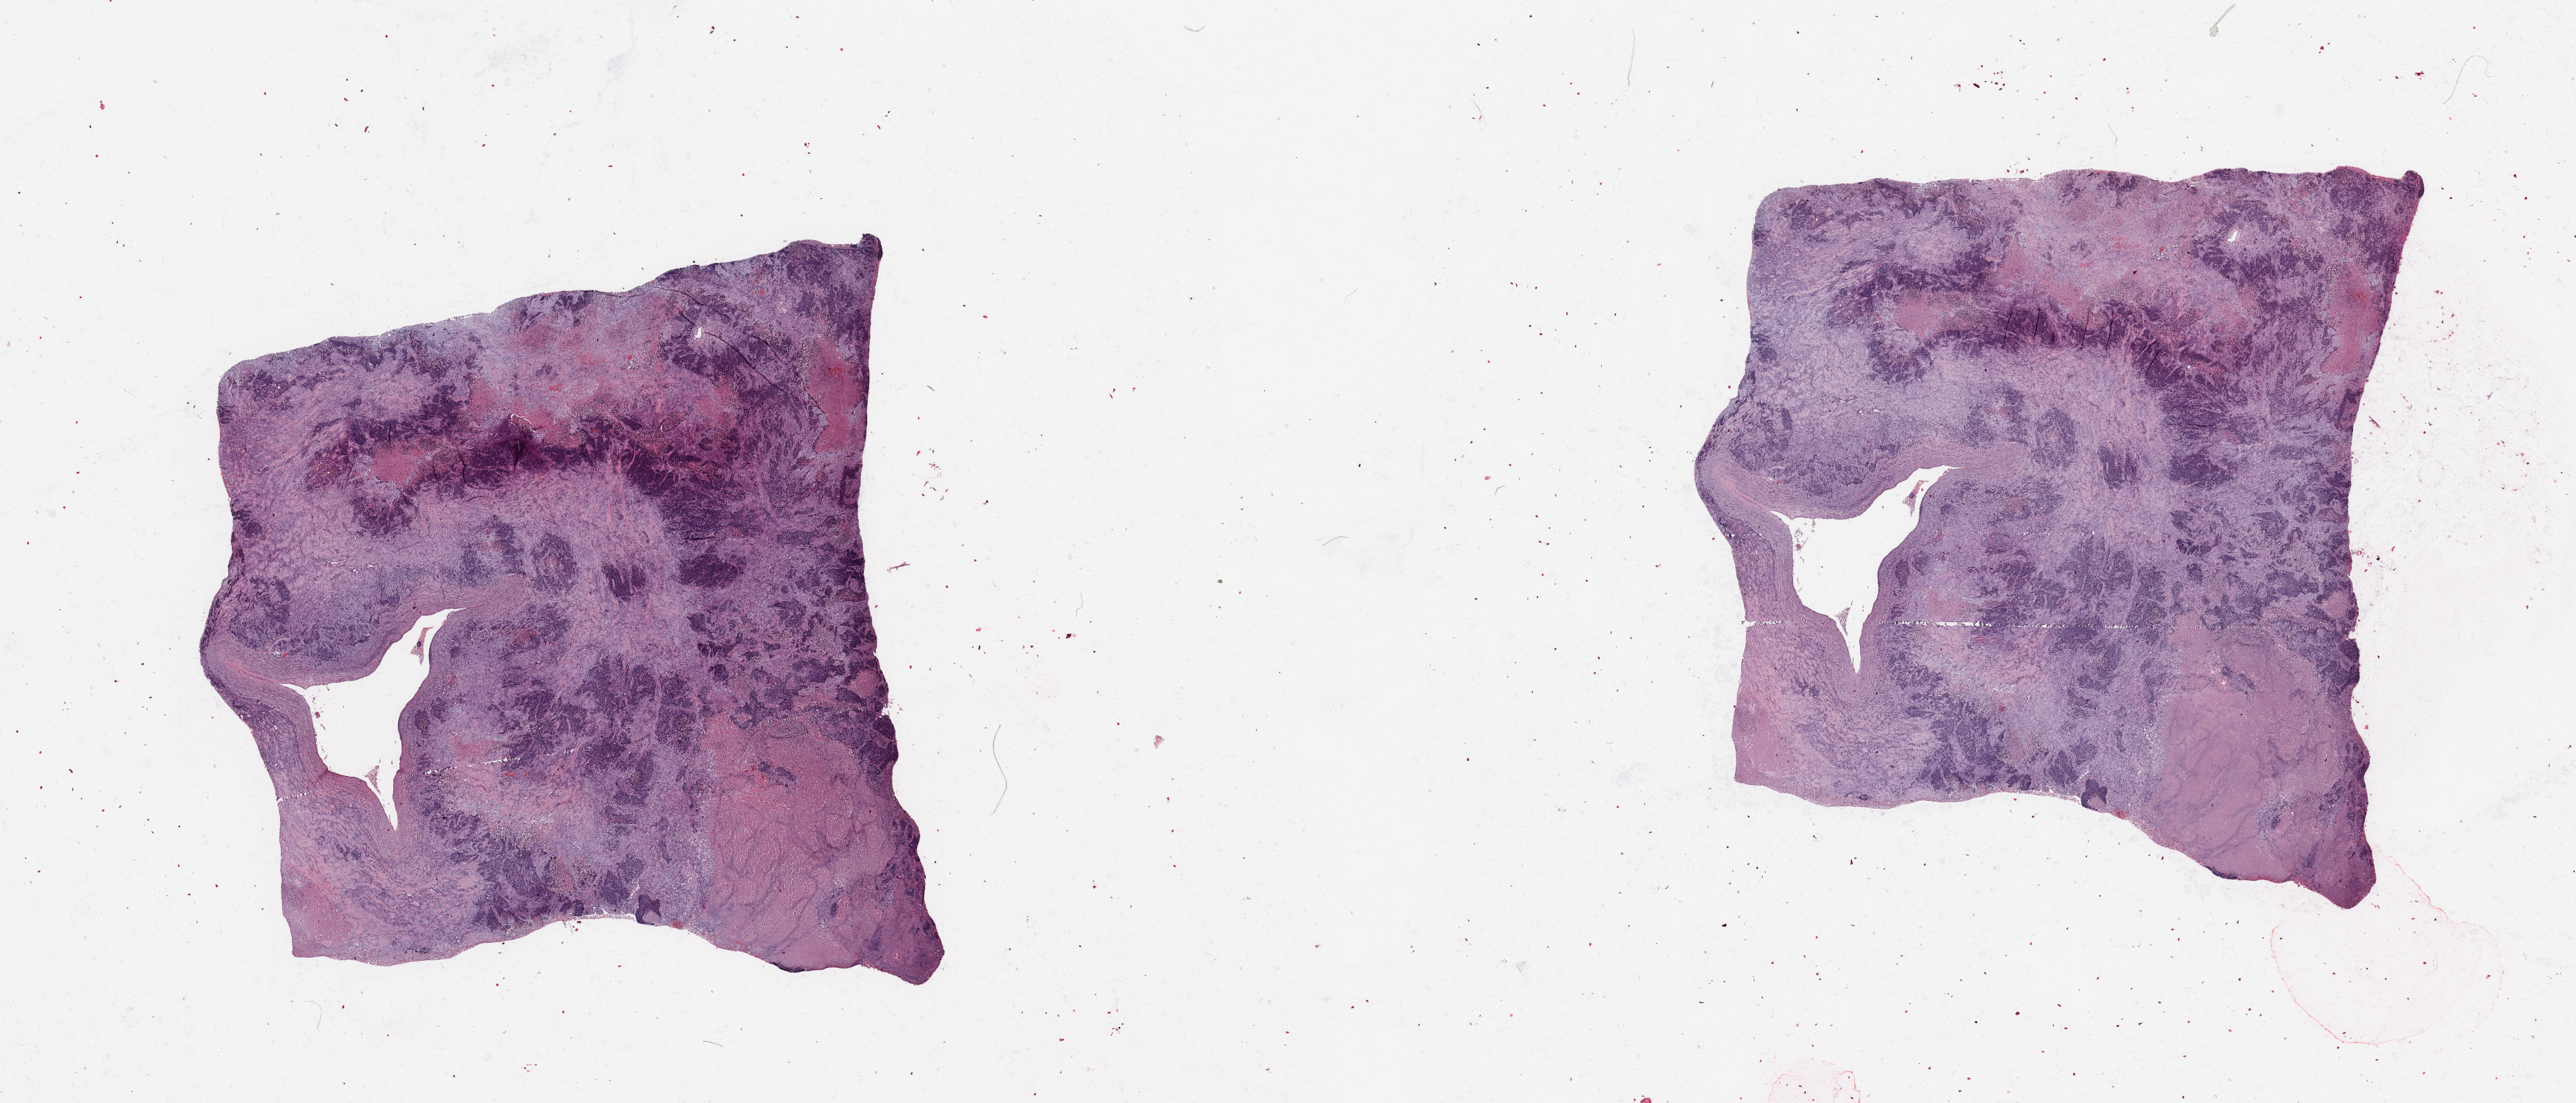
Whole-slide histology image, H&E, a low-resolution overview of the entire scanned area, about 29.5 x 12.6 mm (acquisition: 20x scan), tumour tissue sample, lung. Patient: male, age 54 years. Histologic grade: G2 (moderately differentiated).
Diagnosis: Squamous cell carcinoma, NOS. AJCC pathologic stage: IIIA.